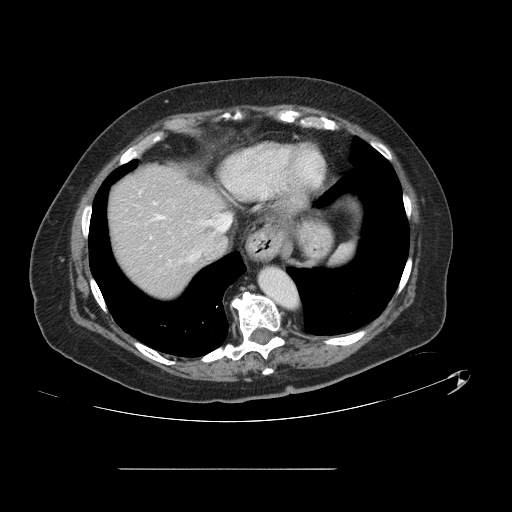
Contrast-enhanced abdominal CT, one axial slice. Slice 116 of 148 in the series (ordered by position). 120 kVp. Soft-tissue window (W 400 / L 40 HU). 2.5 mm slice thickness. 512 × 512 image matrix. Female patient, age 75 years. Case-level facts recorded for this patient, not image findings: diagnosis: colorectal cancer liver metastases, imaged before liver resection; multiple liver metastases: no; largest metastasis: 2.4 cm.
Annotated regions visible in this slice (expert manual segmentation):
- hepatic veins: bounding box <156,214,232,261> (left, top, right, bottom; pixels)
- liver: <108,166,224,297>
- planned liver remnant (the part of the liver to remain after resection): <108,166,224,297>